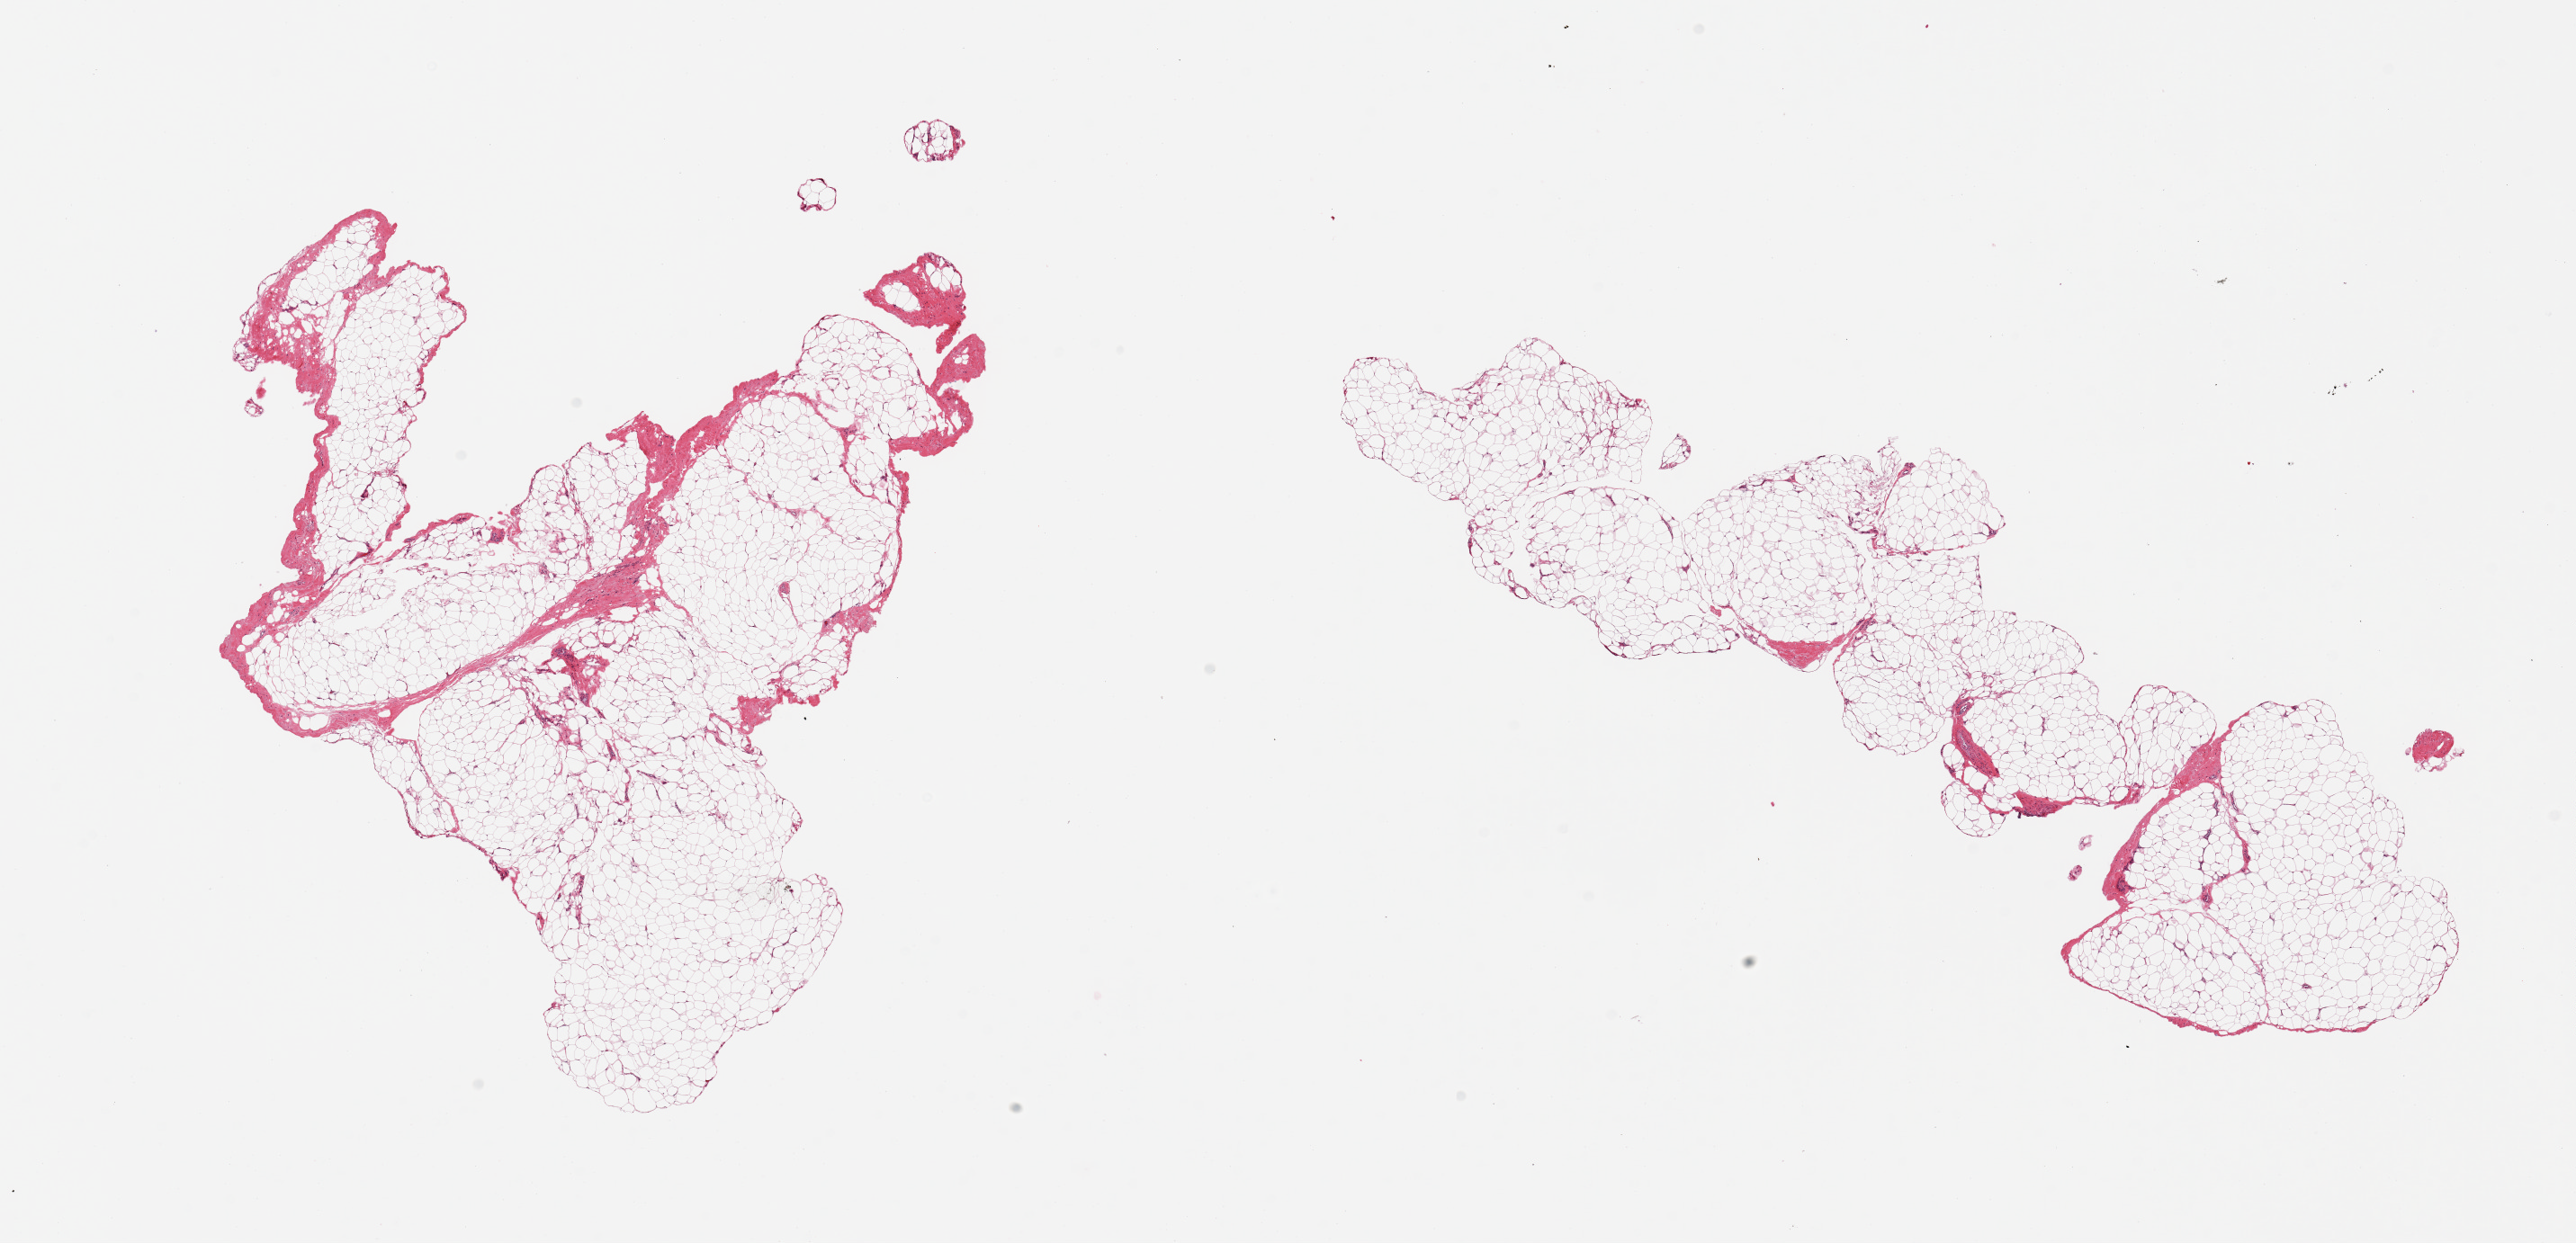
Hematoxylin and eosin (H&E) whole-slide image, shown as a low-resolution overview of the whole scanned area (about 22.6 x 10.9 mm); PAXgene-fixed paraffin-embedded (PFPE) section; section of adipose tissue (target tissue); donor tissue sample. Donor sex: male.
Pathologist's review note for this sample: 2 pieces; no more than 10% fibrovasular component.